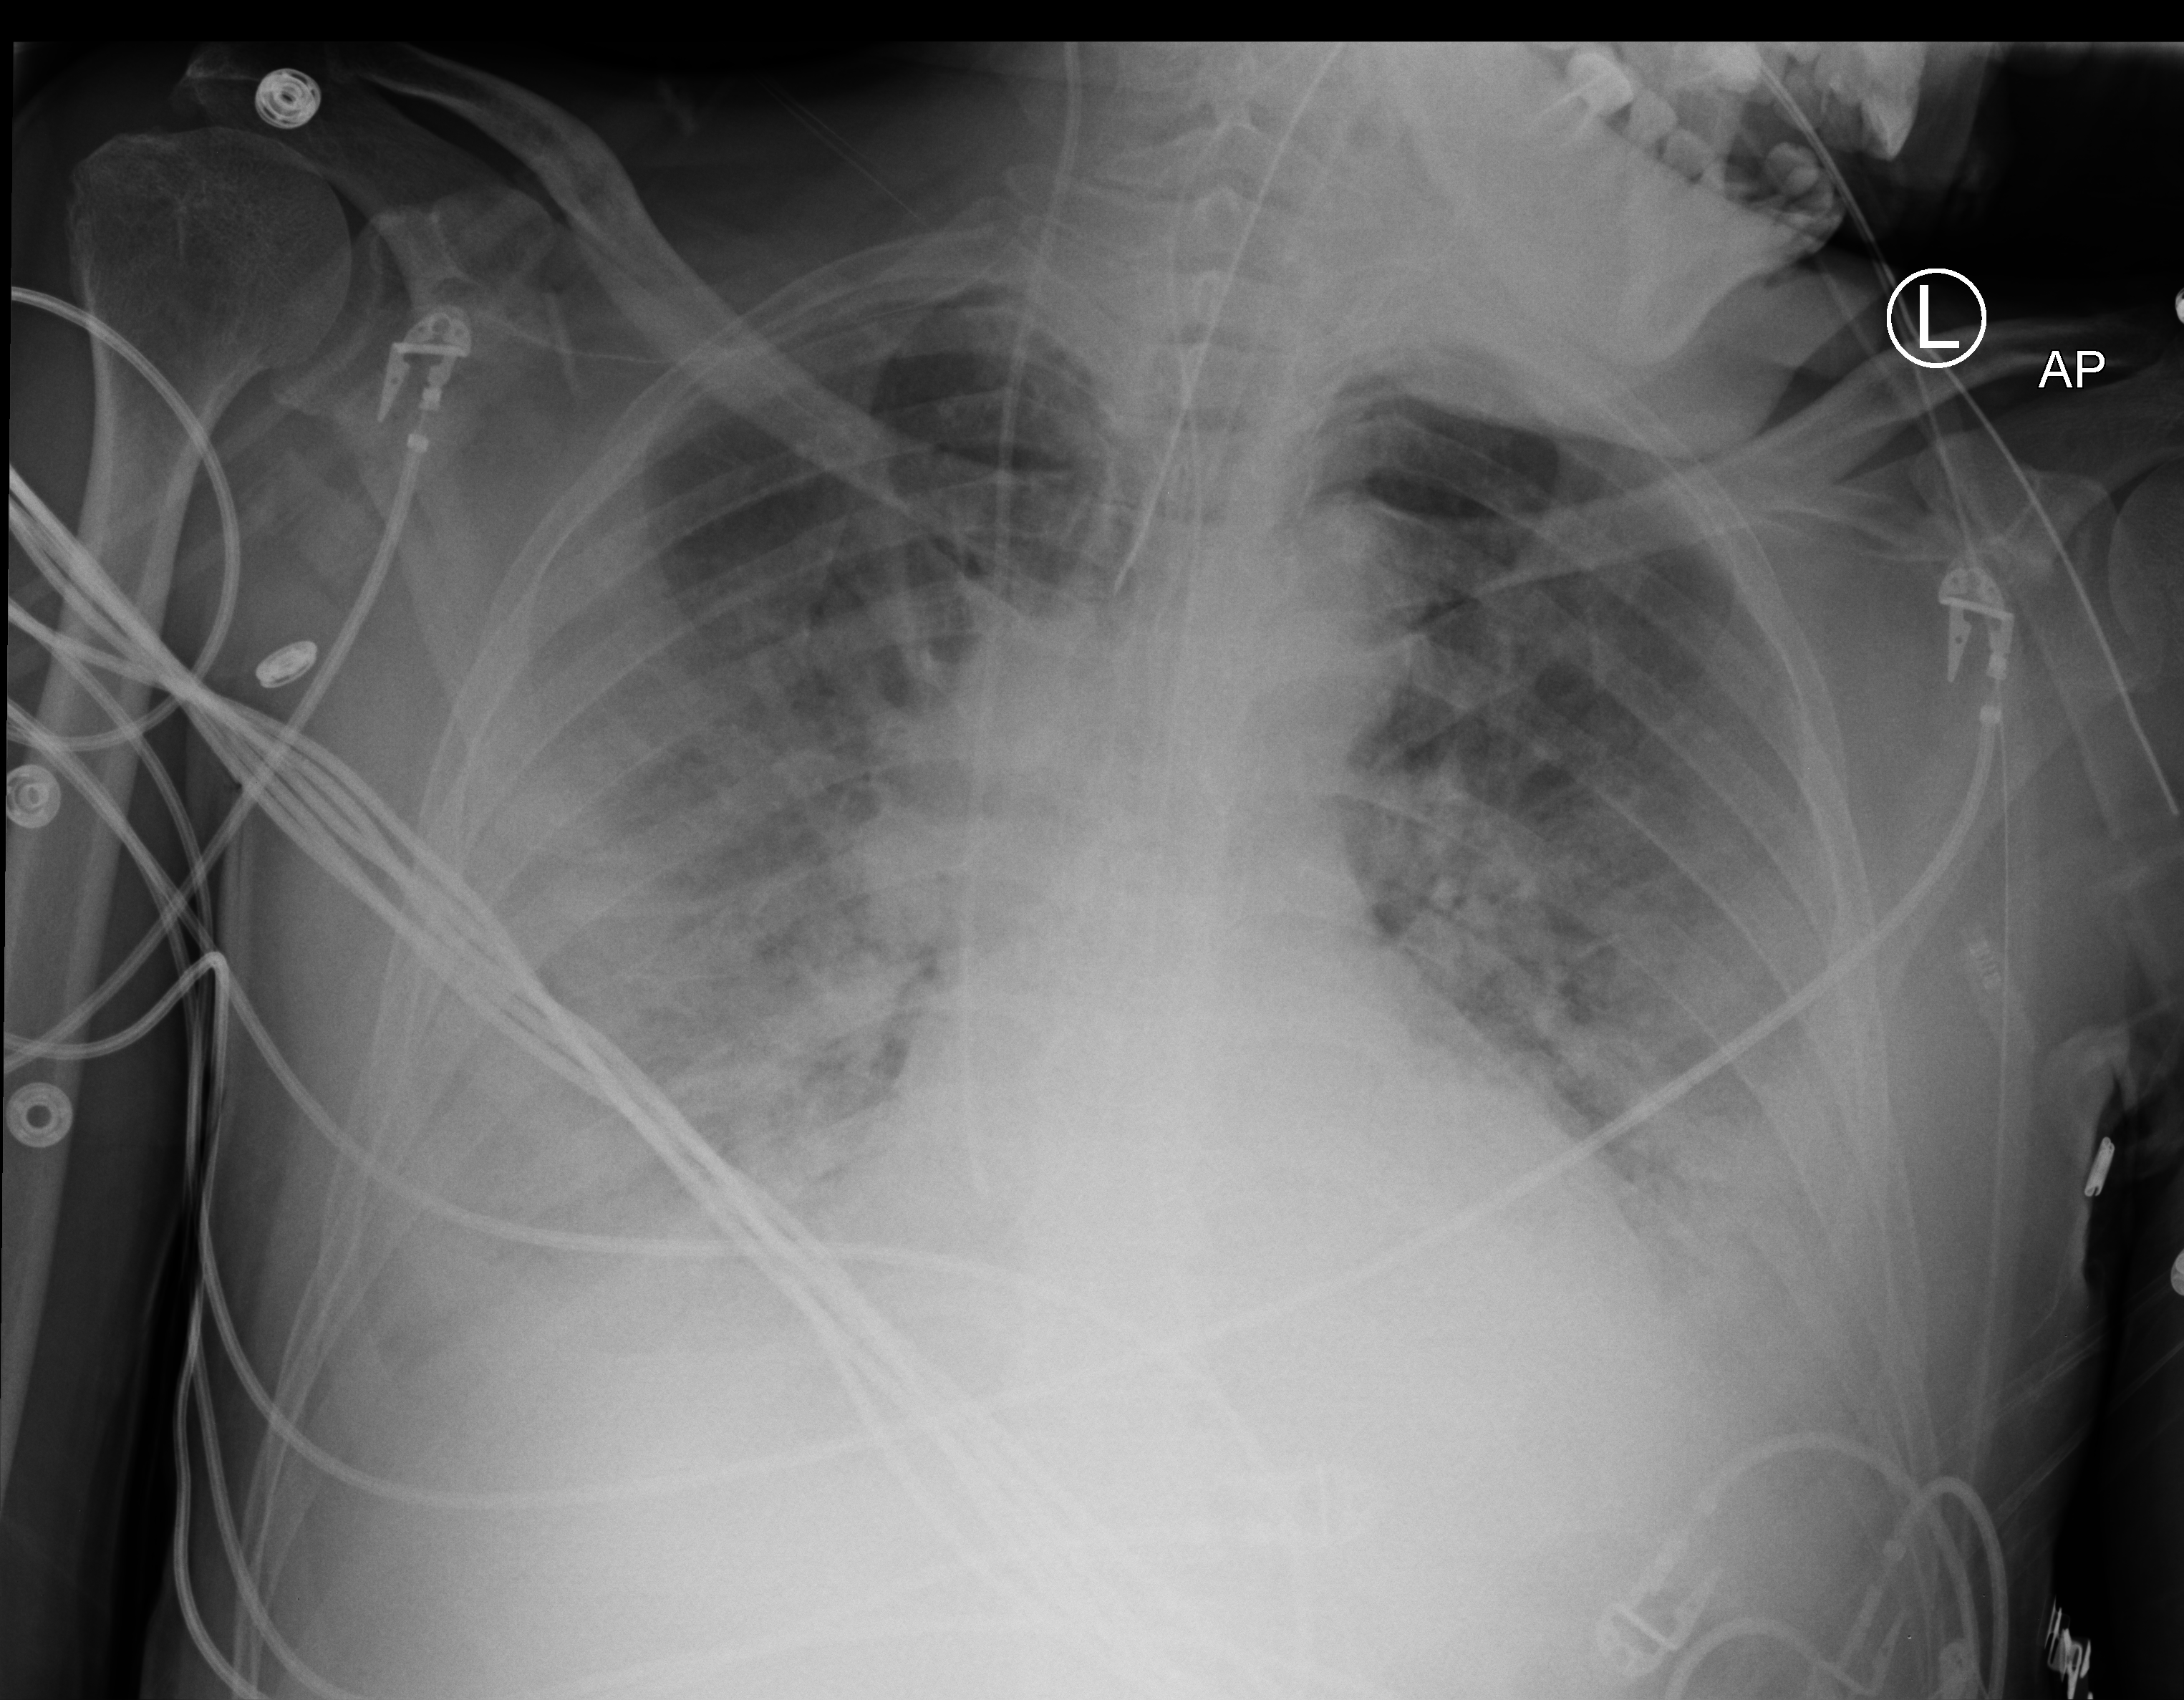
Chest X-ray (portable), anteroposterior (AP) projection. Male patient hospitalised with COVID-19, age 18–59 years.
From the hospital-stay record, not from the radiograph (when in the stay this image was taken is not recorded): mechanically ventilated during this hospital stay: yes; smoking status (admission record): never.